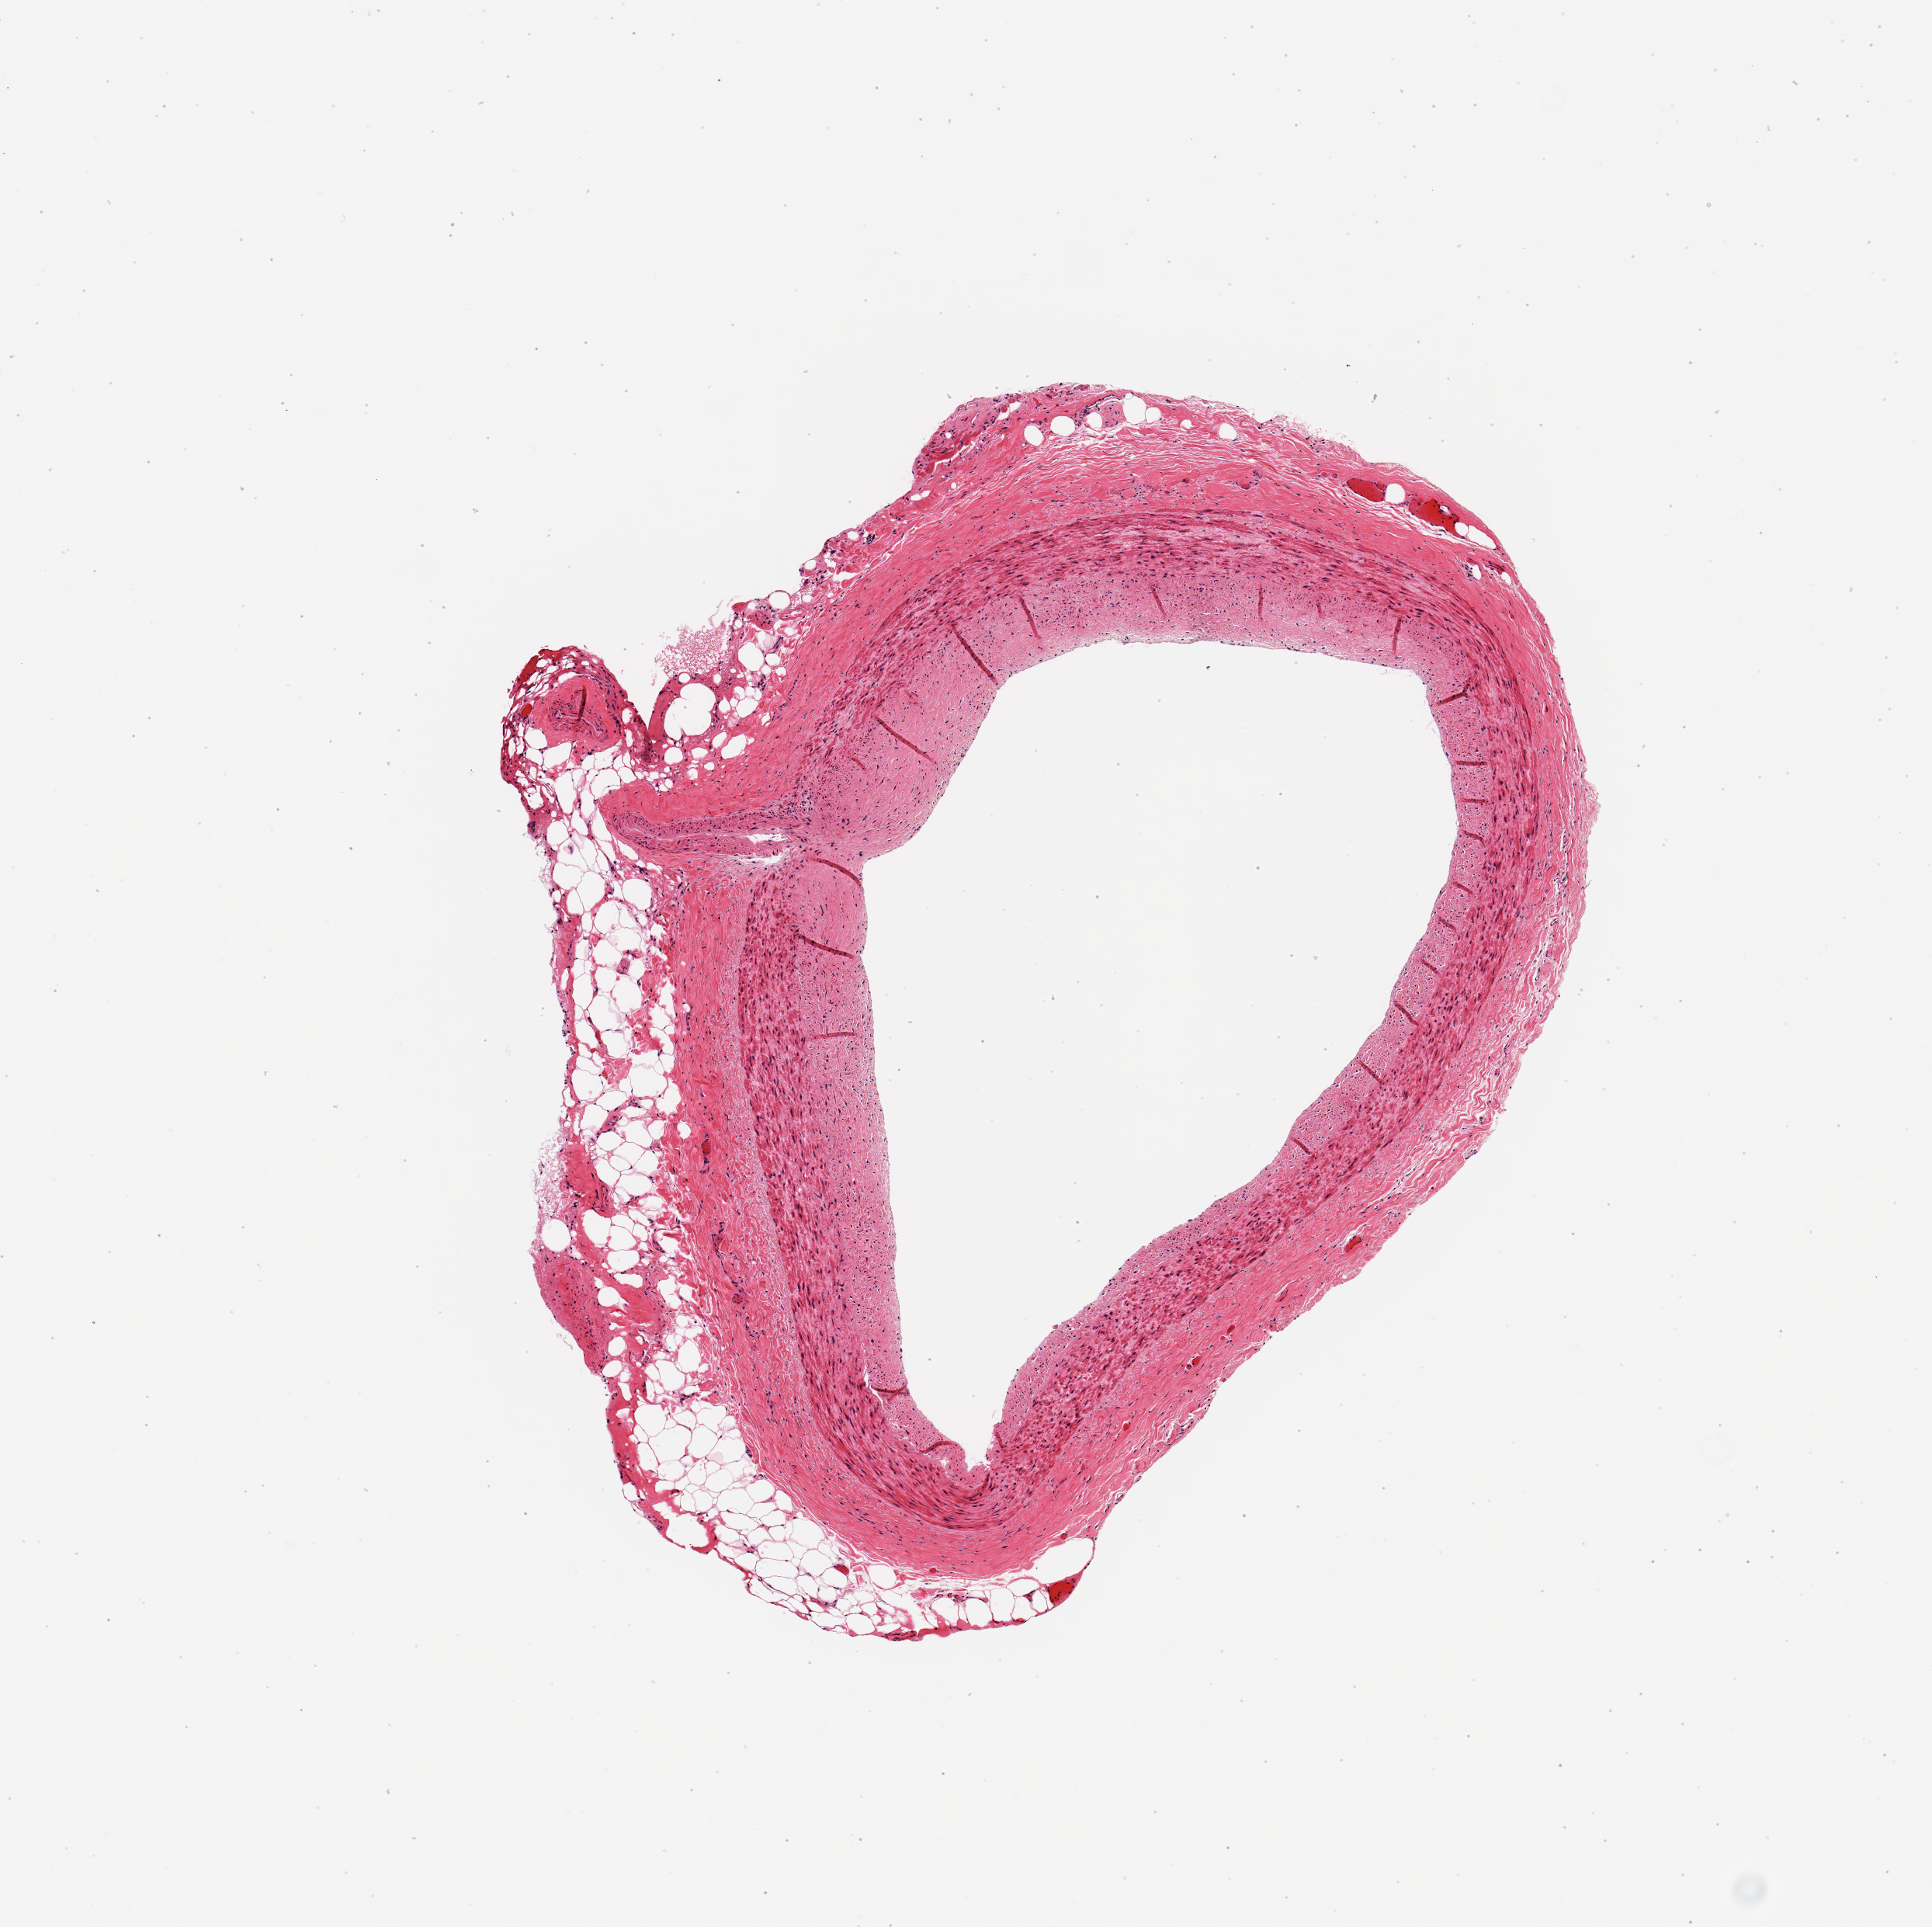
Digitized haematoxylin and eosin-stained section, brightfield, a low-resolution overview of the entire scanned area, about 4.9 x 4.9 mm (slide scanned at 20x), PAXgene-fixed paraffin-embedded (PFPE) section, section of coronary artery (target tissue), donor tissue sample. Female donor.
Review note (as recorded): 1 piece; small rim of fat (~25%).